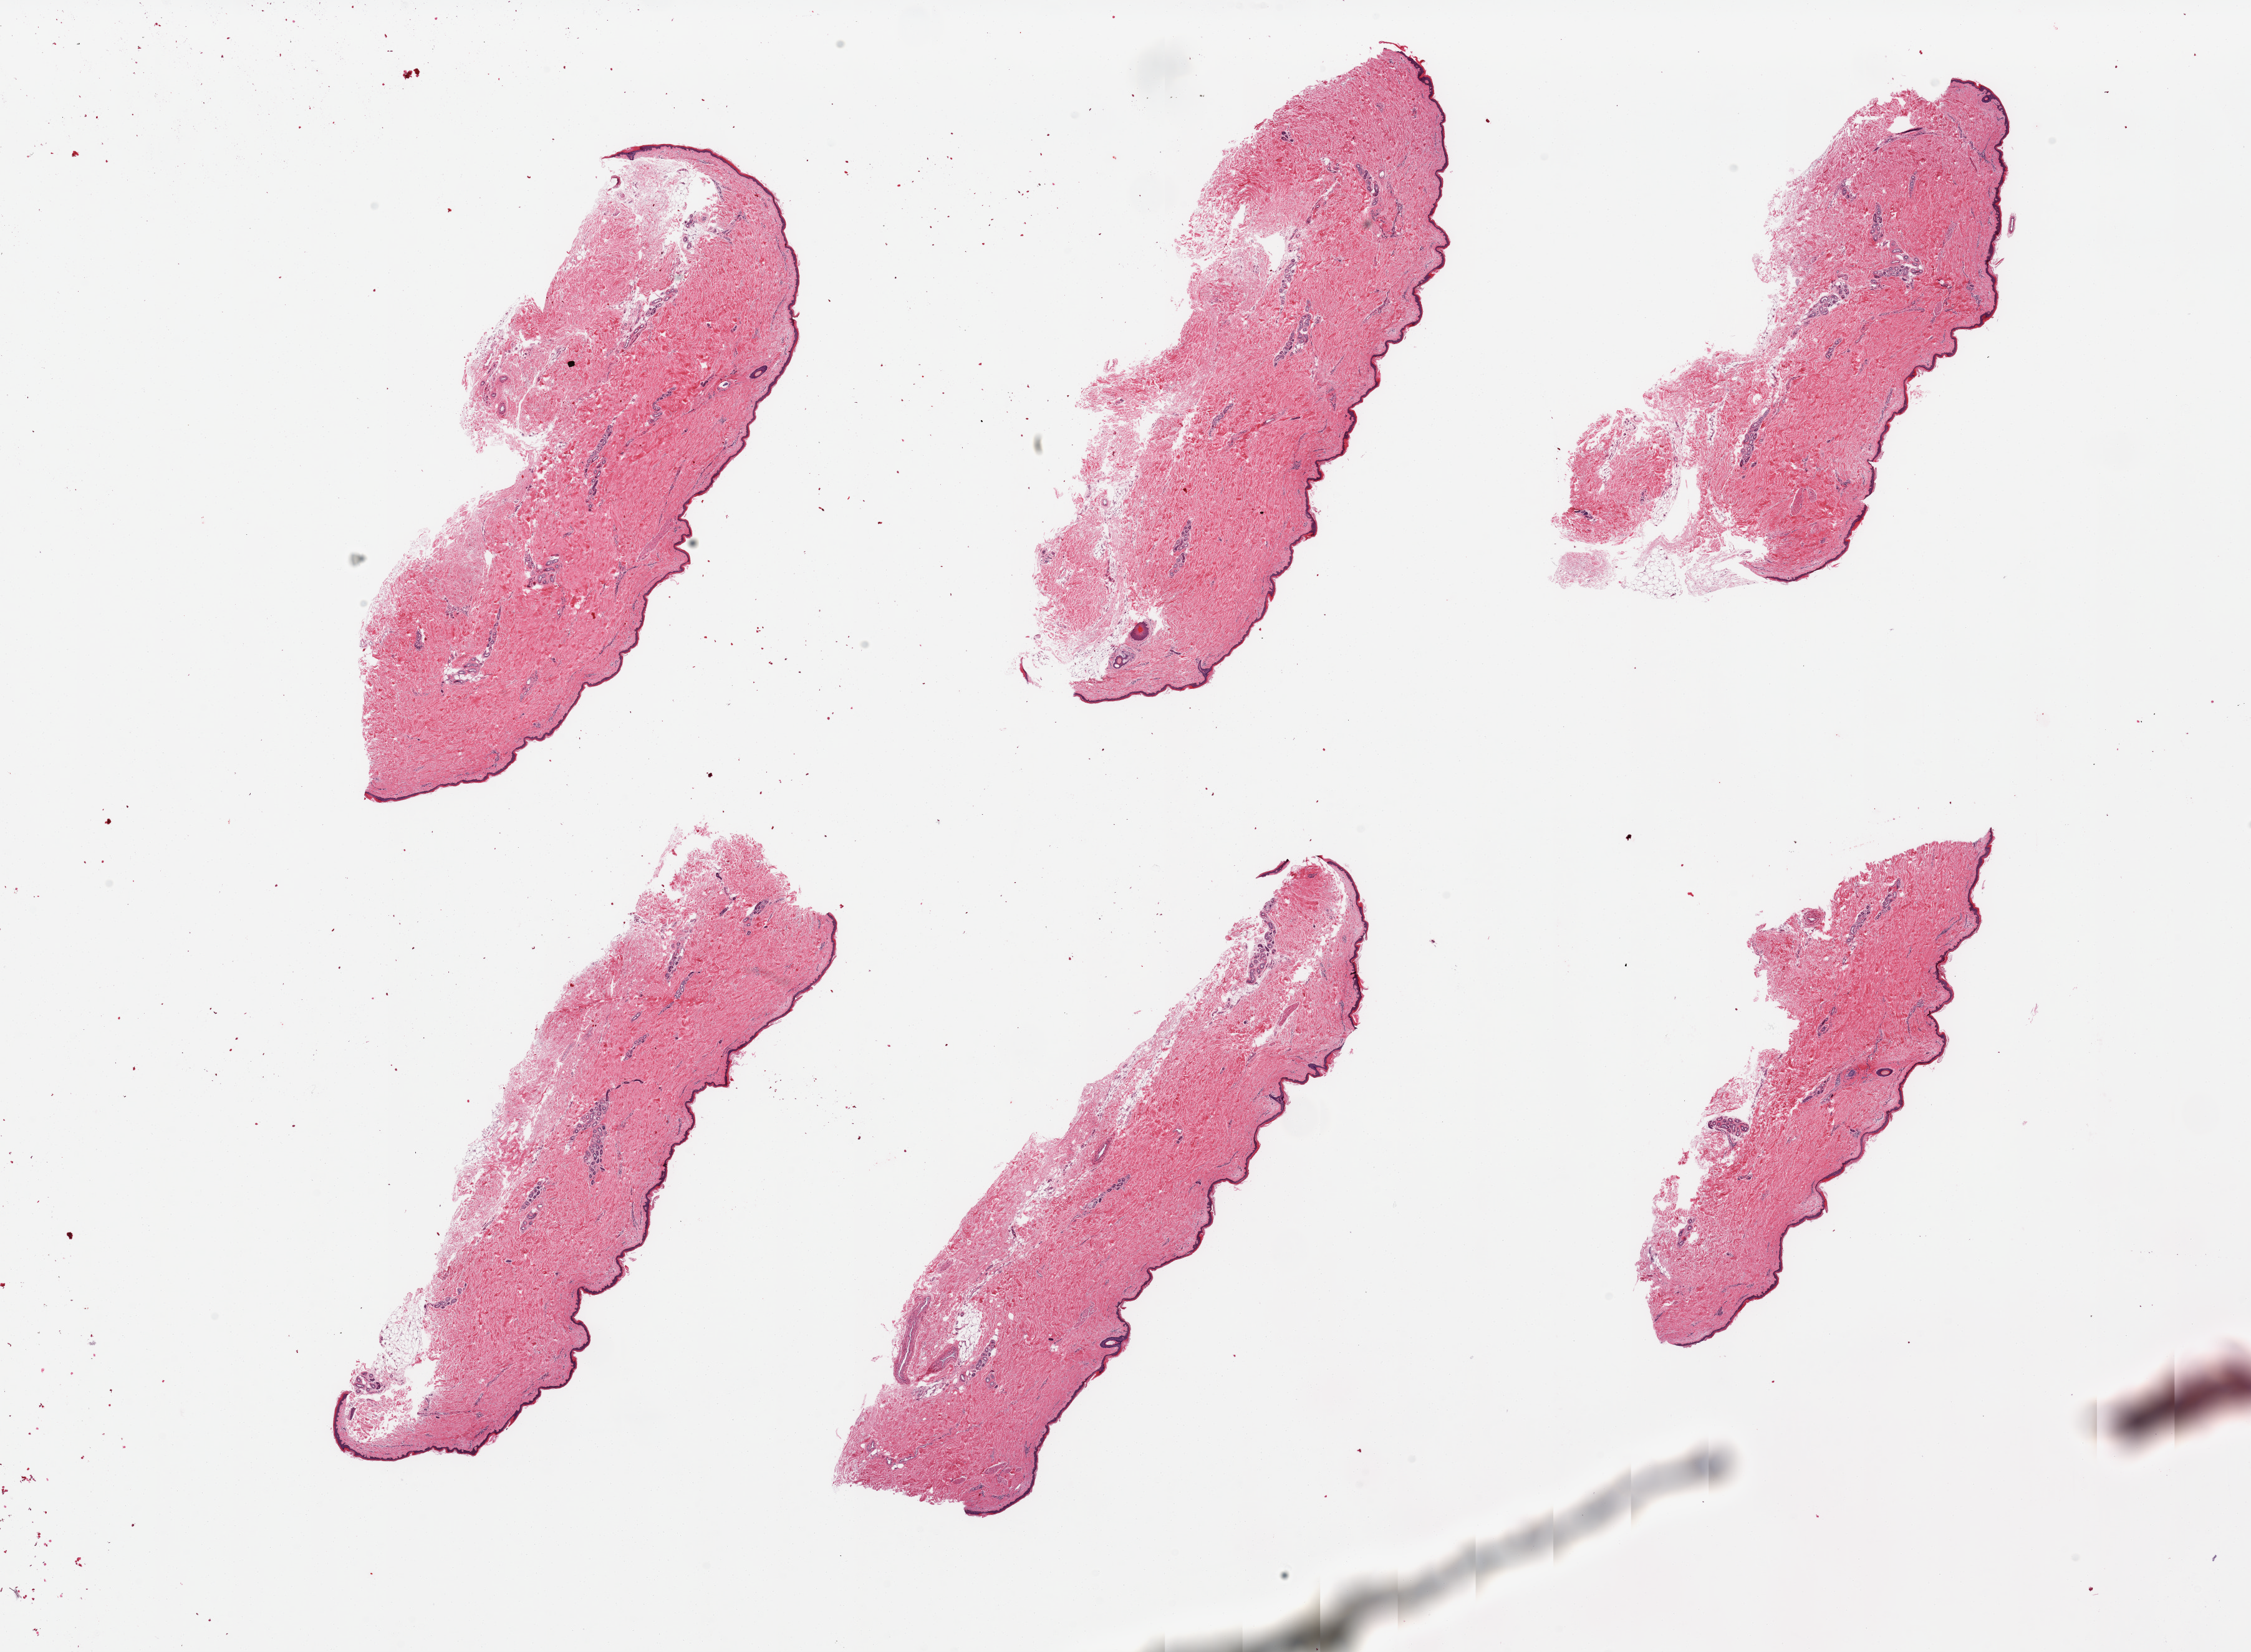
Haematoxylin and eosin whole-slide image, low-resolution overview of the scanned area, about 28.5 x 21.0 mm (from a 20x scan), PAXgene-fixed paraffin-embedded (PFPE) section, target tissue: skin of lower leg, tissue donor sample. Male donor.
Reviewer comment on this tissue sample: 6 pieces; well trimmed with <10% attached and internal fat, epidermis measures 26 microns.